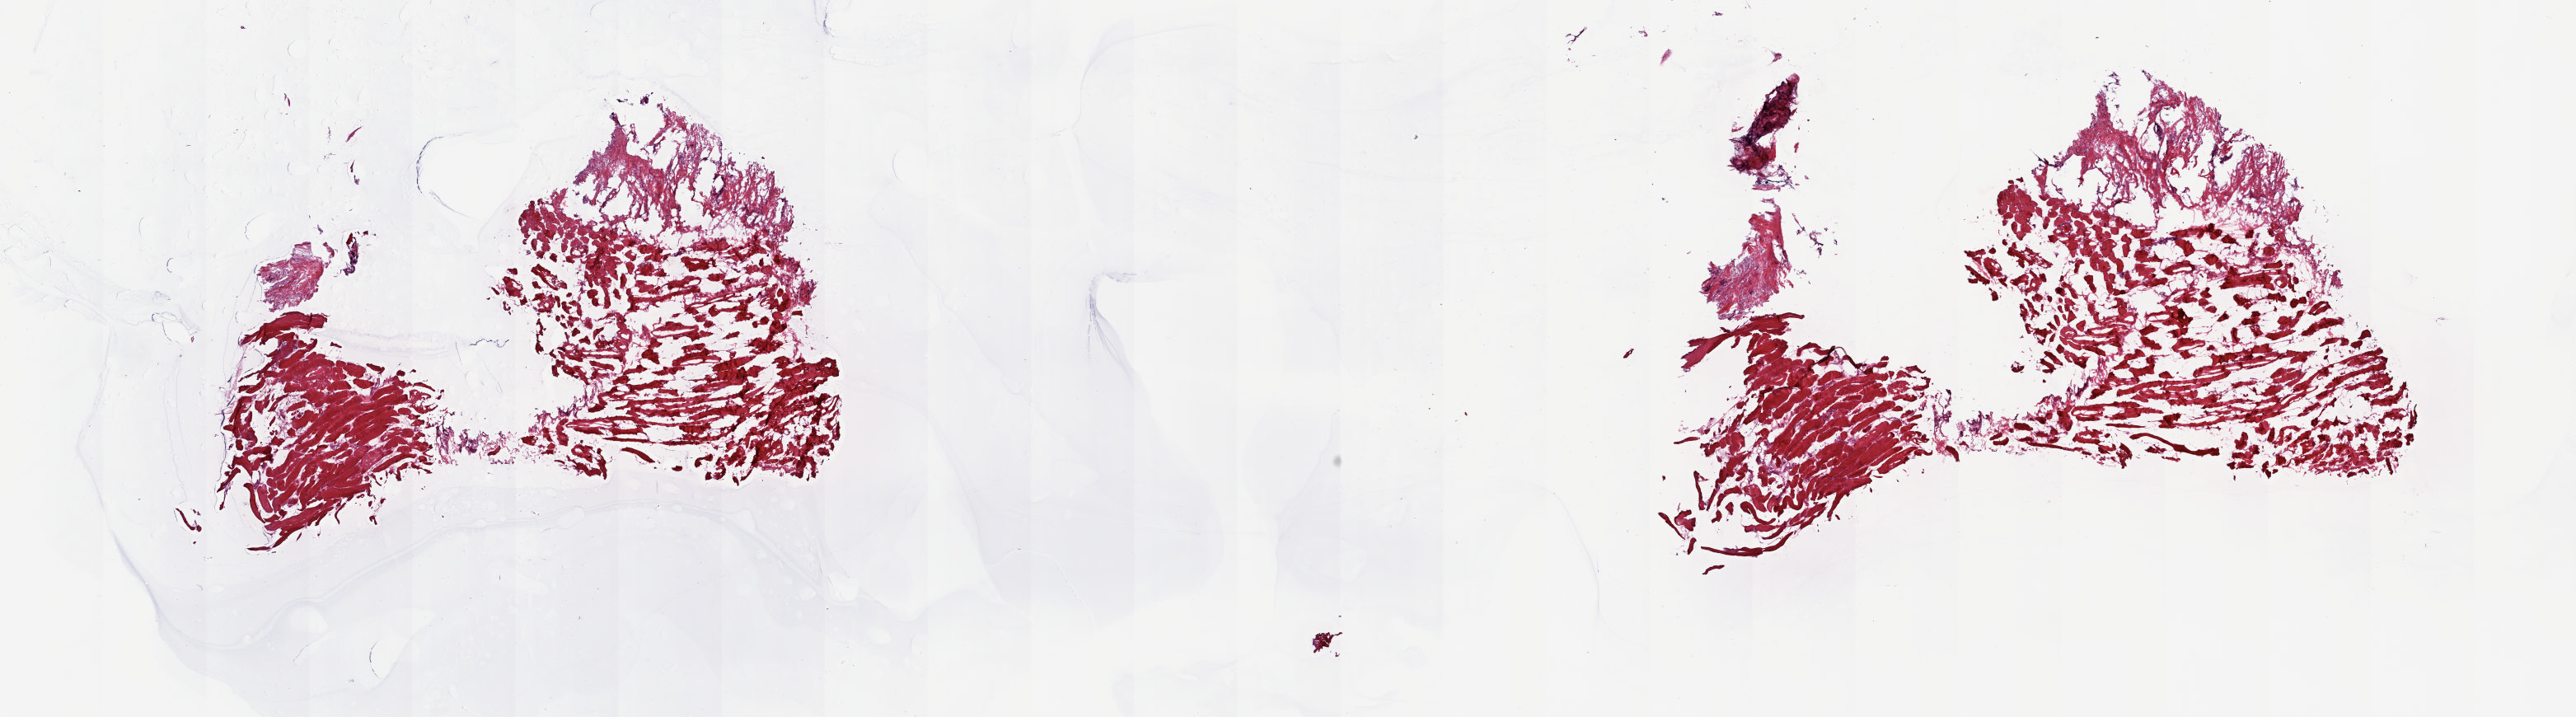
H&E-stained whole-slide image, whole scanned area (about 24.8 x 6.9 mm, acquisition: 20x scan) shown as a low-resolution overview; frozen section from the top of the tissue portion; solid tissue normal (non-tumour tissue) sample from the connective, subcutaneous and other soft tissues. Male, age 86 years at initial diagnosis. Composition of this section per pathologist review: tumour cells 0%, tumour nuclei 0%, normal cells 100%, stromal cells 0%, necrosis 0%. Inflammatory infiltration, as recorded: lymphocyte infiltration 0%, monocyte infiltration 0%, neutrophil infiltration 0%.
This section: solid tissue normal (non-tumour) sample from the same patient. Patient diagnosis: Undifferentiated sarcoma (connective, subcutaneous and other soft tissues of trunk, NOS).